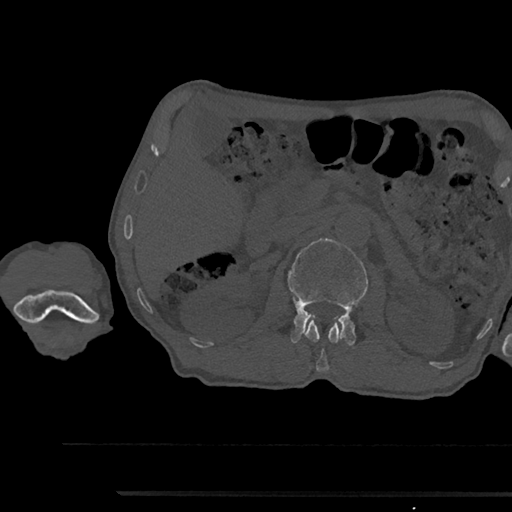
CT including the spine, one axial slice. Slice 597 of 797 in the series (ordered by position). Reconstruction kernel Br40s/3. Bone window (W 1800 / L 400 HU). 0.5 mm slice thickness. 512 × 512 image matrix, field of view 367 × 367 mm. Male patient, age 79 years. Case-level facts recorded for this patient, not image findings: primary cancer: prostate.
Structures marked on this image (semi-automatic segmentation, software-assisted and operator-edited):
- L1 vertebra: box from (x=305, y=319) to (x=343, y=371) px
- L2 vertebra: (x=288, y=238)–(x=368, y=345)